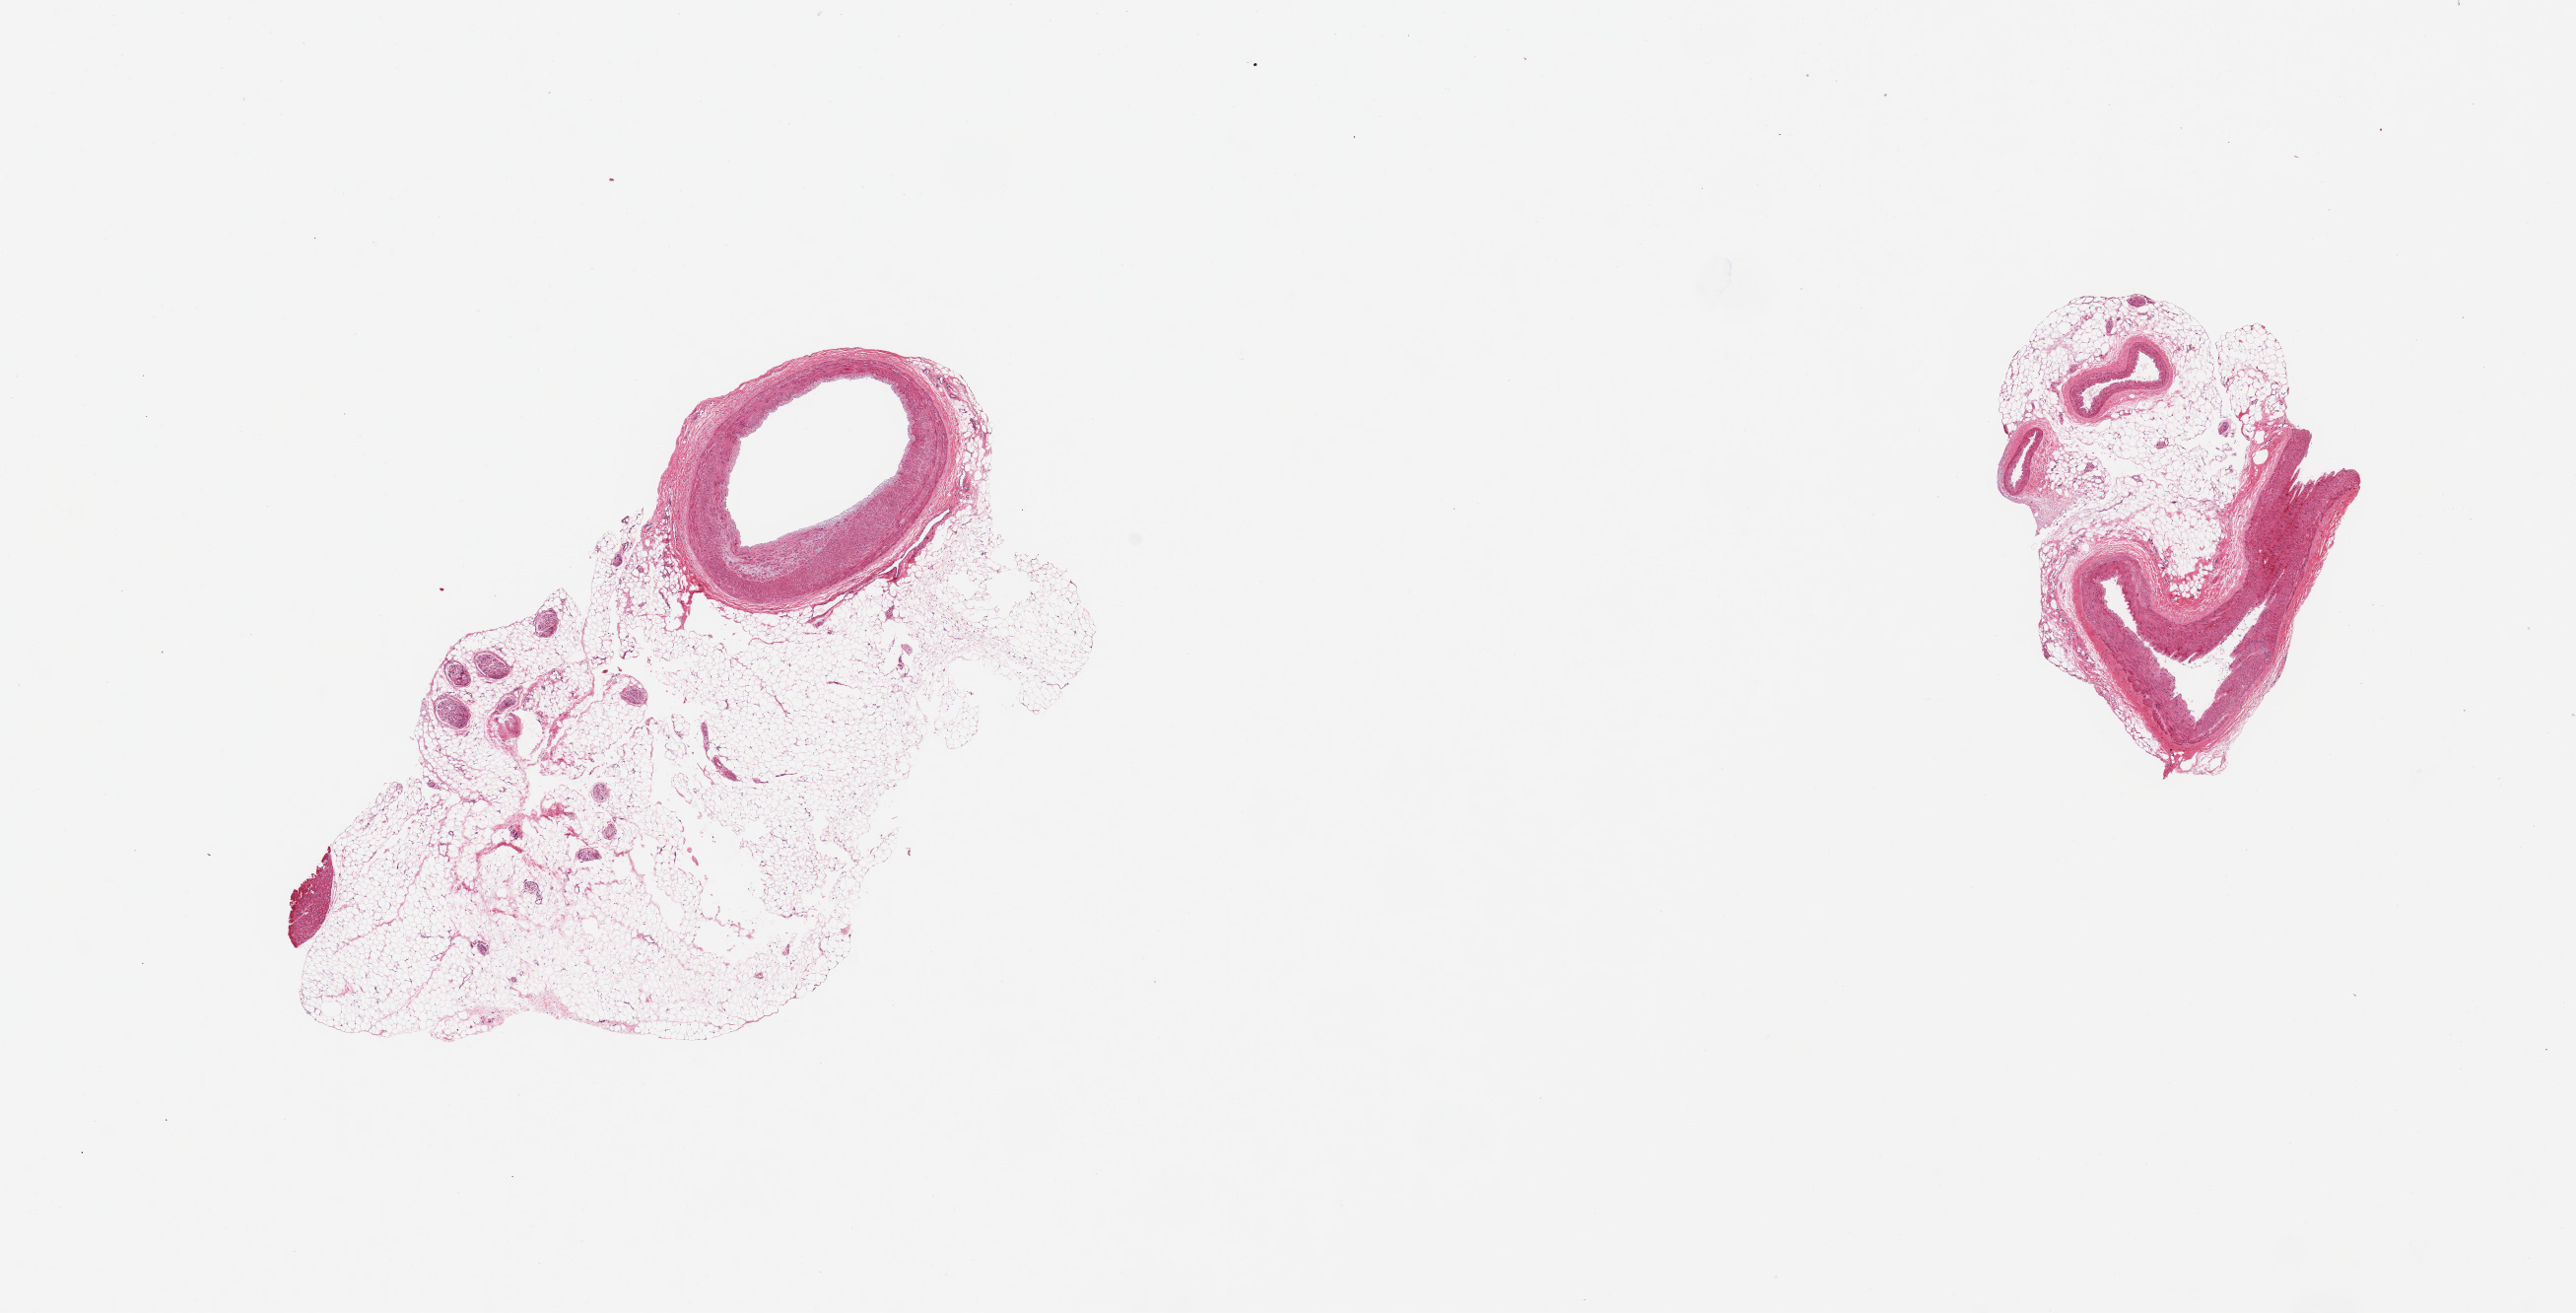
Digitized haematoxylin and eosin-stained section, brightfield, whole scanned area (about 20.7 x 10.5 mm, slide scanned at 20x) shown as a low-resolution overview, PAXgene-fixed paraffin-embedded (PFPE) section, target tissue: coronary artery, tissue donor sample. Donor sex: female.
- reviewer comment on this tissue sample: 2 pieces, 7x4 & 3.5x3mm; 40 and 60% adjacent adipose